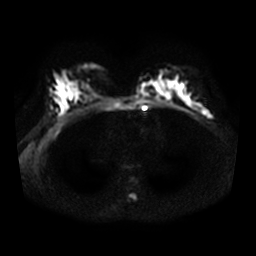
Breast MRI, one axial slice. Diffusion-weighted series; image 2 of 4 stored at this slice position (different b-values; order by instance number). 3 T. 5 mm slice thickness. 256 × 256 image matrix. Female patient.
Annotated regions visible in this slice (manually delineated by an expert):
- tumour on diffusion-weighted imaging: box from (x=203, y=110) to (x=211, y=118) px